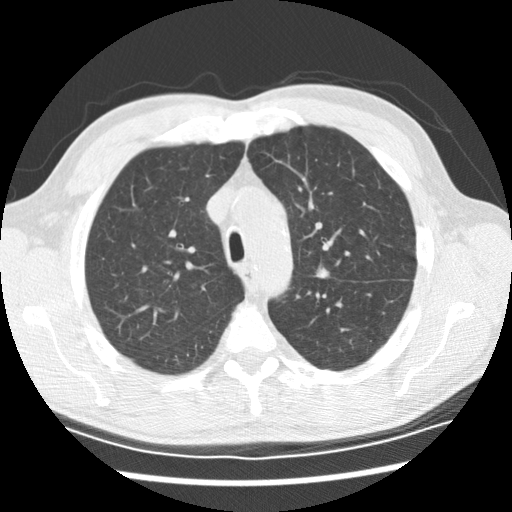
Low-dose screening chest CT, one axial slice; slice 151 of 208 in the series (ordered by position); 120 kVp; lung window (W 1500 / L -600 HU); 2.5 mm slice thickness; 512 × 512 image matrix, field of view 340 × 340 mm.
Annotated regions visible in this slice (expert manual segmentation):
- lesion 1 (tumor, upper lobe of left lung): box from (x=316, y=266) to (x=329, y=278) px